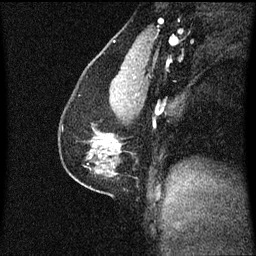
Breast MRI (dynamic contrast-enhanced), one sagittal slice; slice 34 of 60 in the series (ordered by position); dynamic contrast-enhanced series, image 2 of 3 at this slice position (ordered by acquisition); 1.5 T; TE 4.2 ms, TR 8.4 ms; 2 mm slice thickness; 256 × 256 image matrix. Female patient, age 41 years. From the clinical record (not read from this slice): setting: breast cancer imaged before/during neoadjuvant chemotherapy; receptor status: triple-negative.
Annotated regions visible in this slice (semi-automatic segmentation, software-assisted and operator-edited):
- analysis volume of interest (the breast-tissue region the enhancement analysis was run in; not a lesion): bounding box [x1, y1, x2, y2] px = [60, 104, 125, 175]
- tumour enhancement mask (voxels above the 70 % enhancement threshold inside the analysis volume of interest): [109, 140, 121, 147]